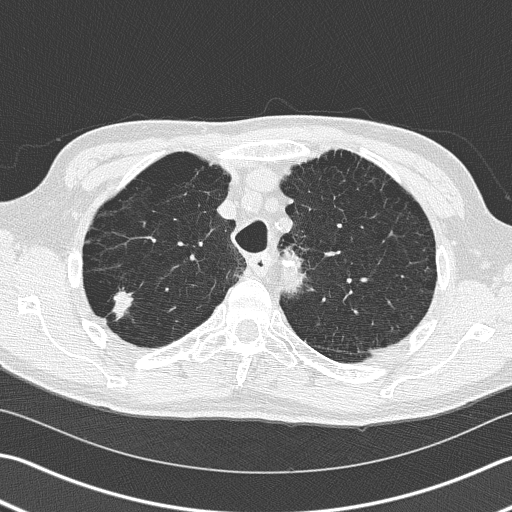
Low-dose screening chest CT, one axial slice; position 124 of 163 along the scan axis; 120 kVp; lung window (W 1500 / L -600 HU); 2 mm slice thickness; 512 × 512 image matrix.
Outlined on this slice (outlined manually by an expert reader):
- lesion 1 (tumor, upper lobe of right lung): box from (x=113, y=291) to (x=133, y=318) px